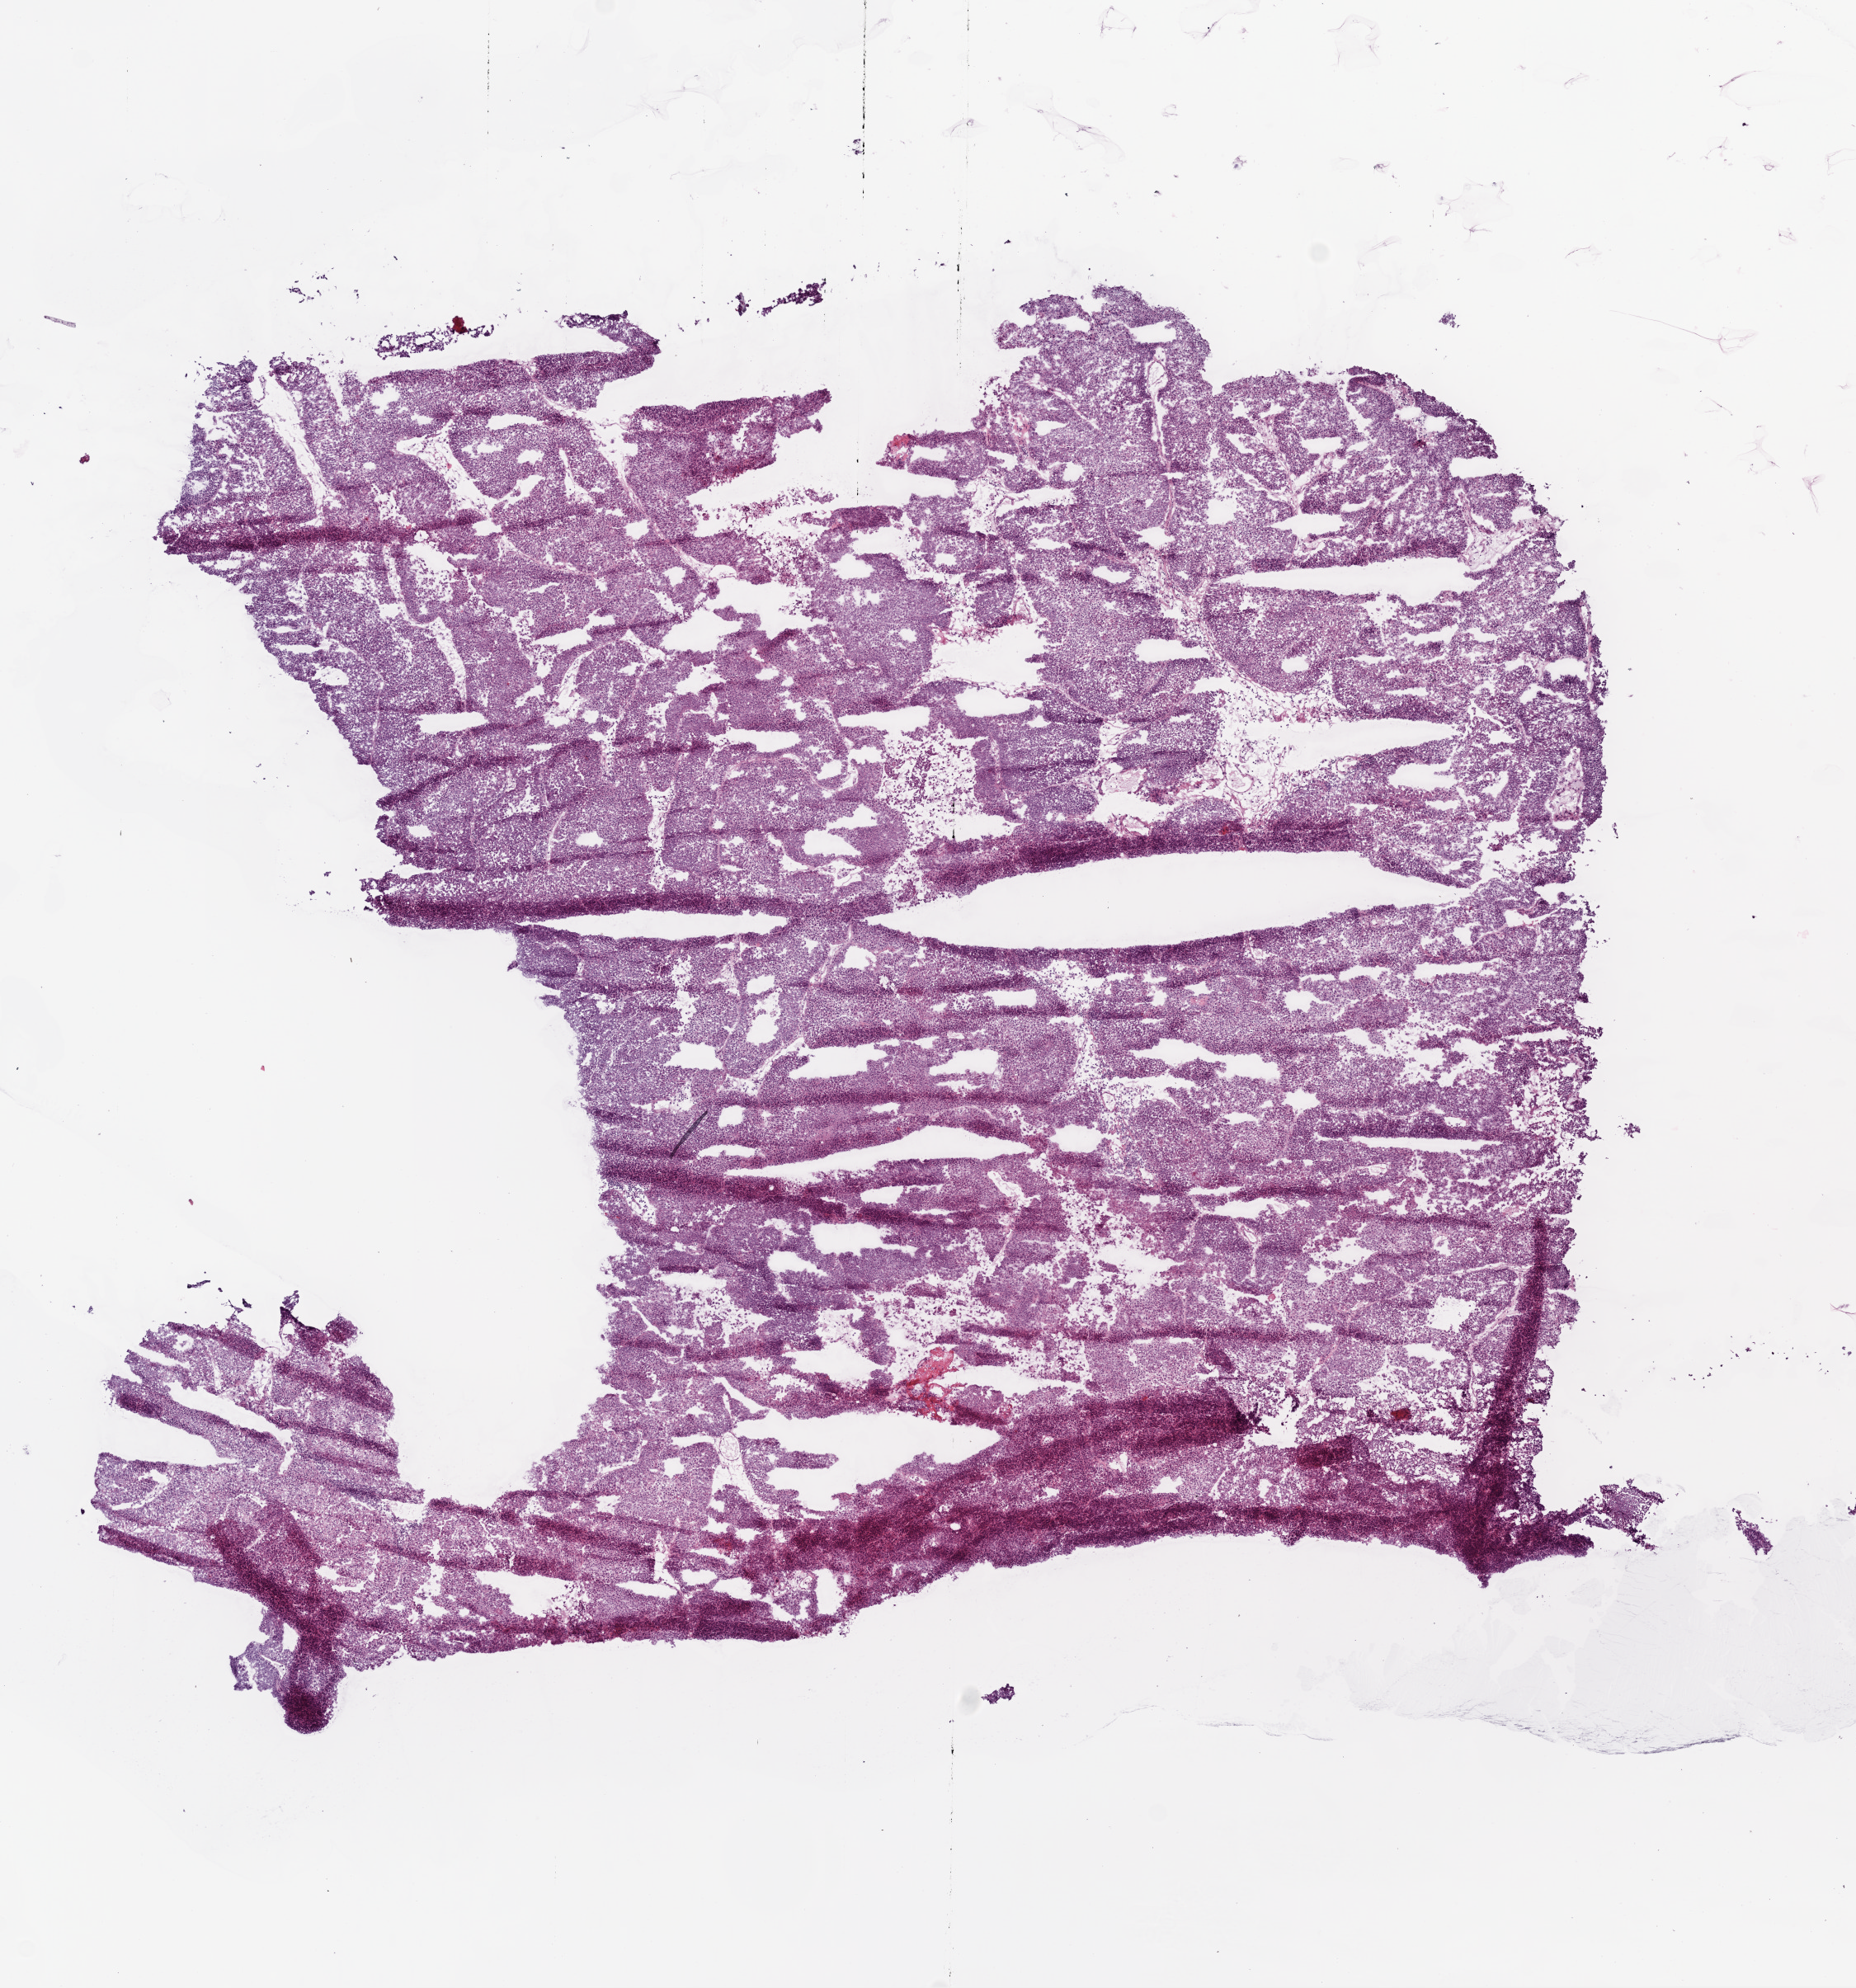
Digitized H&E tissue section (whole slide) — a low-resolution overview of the entire scanned area, about 9.0 x 9.7 mm (acquisition: 20x scan), frozen section from the bottom of the tissue portion, sample: primary tumour, ovary. Female patient; age at initial diagnosis 71 years. Histologic grade: G3 (poorly differentiated). Slide review estimates, as recorded: tumour cells 95%, tumour nuclei 95%, normal cells 1%, stromal cells 4%, necrosis 0%.
Pathologic diagnosis: Serous cystadenocarcinoma, NOS. FIGO stage: IA. Laterality: left.